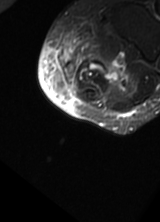
MRI of an extremity soft-tissue mass, one axial slice; slice 2 of 69 in the series (ordered by position); T2-weighted fat-saturated; MR volume resampled by the dataset authors to the PET/CT grid (not the native acquisition matrix); 3.27 mm slice thickness; 160 × 222 image matrix, field of view 156 × 217 mm. Female patient. From the clinical record (not read from this slice): histological type: pleomorphic leiomyosarcoma; grade: high; site of the primary tumour: left thigh.
Structures marked on this image (expert contour drawn on MRI and transferred to this co-registered scan by the dataset authors):
- gross tumour volume including surrounding oedema: bounding box (x1, y1, x2, y2) in pixels: (61, 27, 131, 96)